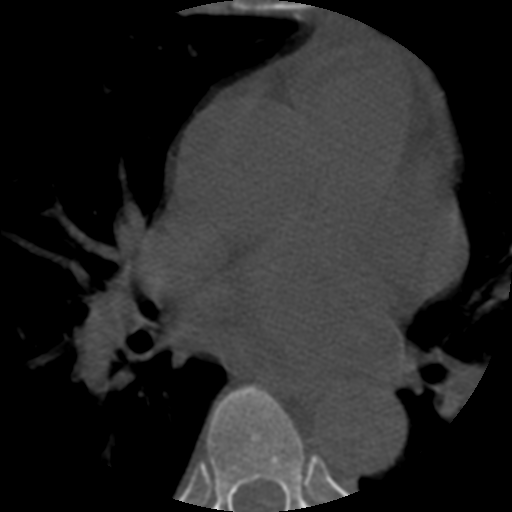
CT including the spine, one axial slice. Slice 360 of 508 in the series (ordered by position). Reconstruction kernel STANDARD. 120 kVp. Bone window (W 1800 / L 400 HU). 1.25 mm slice thickness. 512 × 512 image matrix, field of view 160 × 160 mm. Patient age 57 years. From the clinical record (not read from this slice): primary cancer: prostate.
Structures marked on this image (semi-automatic segmentation, software-assisted and operator-edited):
- T5 vertebra: box from (x=204, y=456) to (x=316, y=466) px
- T6 vertebra: (x=206, y=386)–(x=317, y=512)